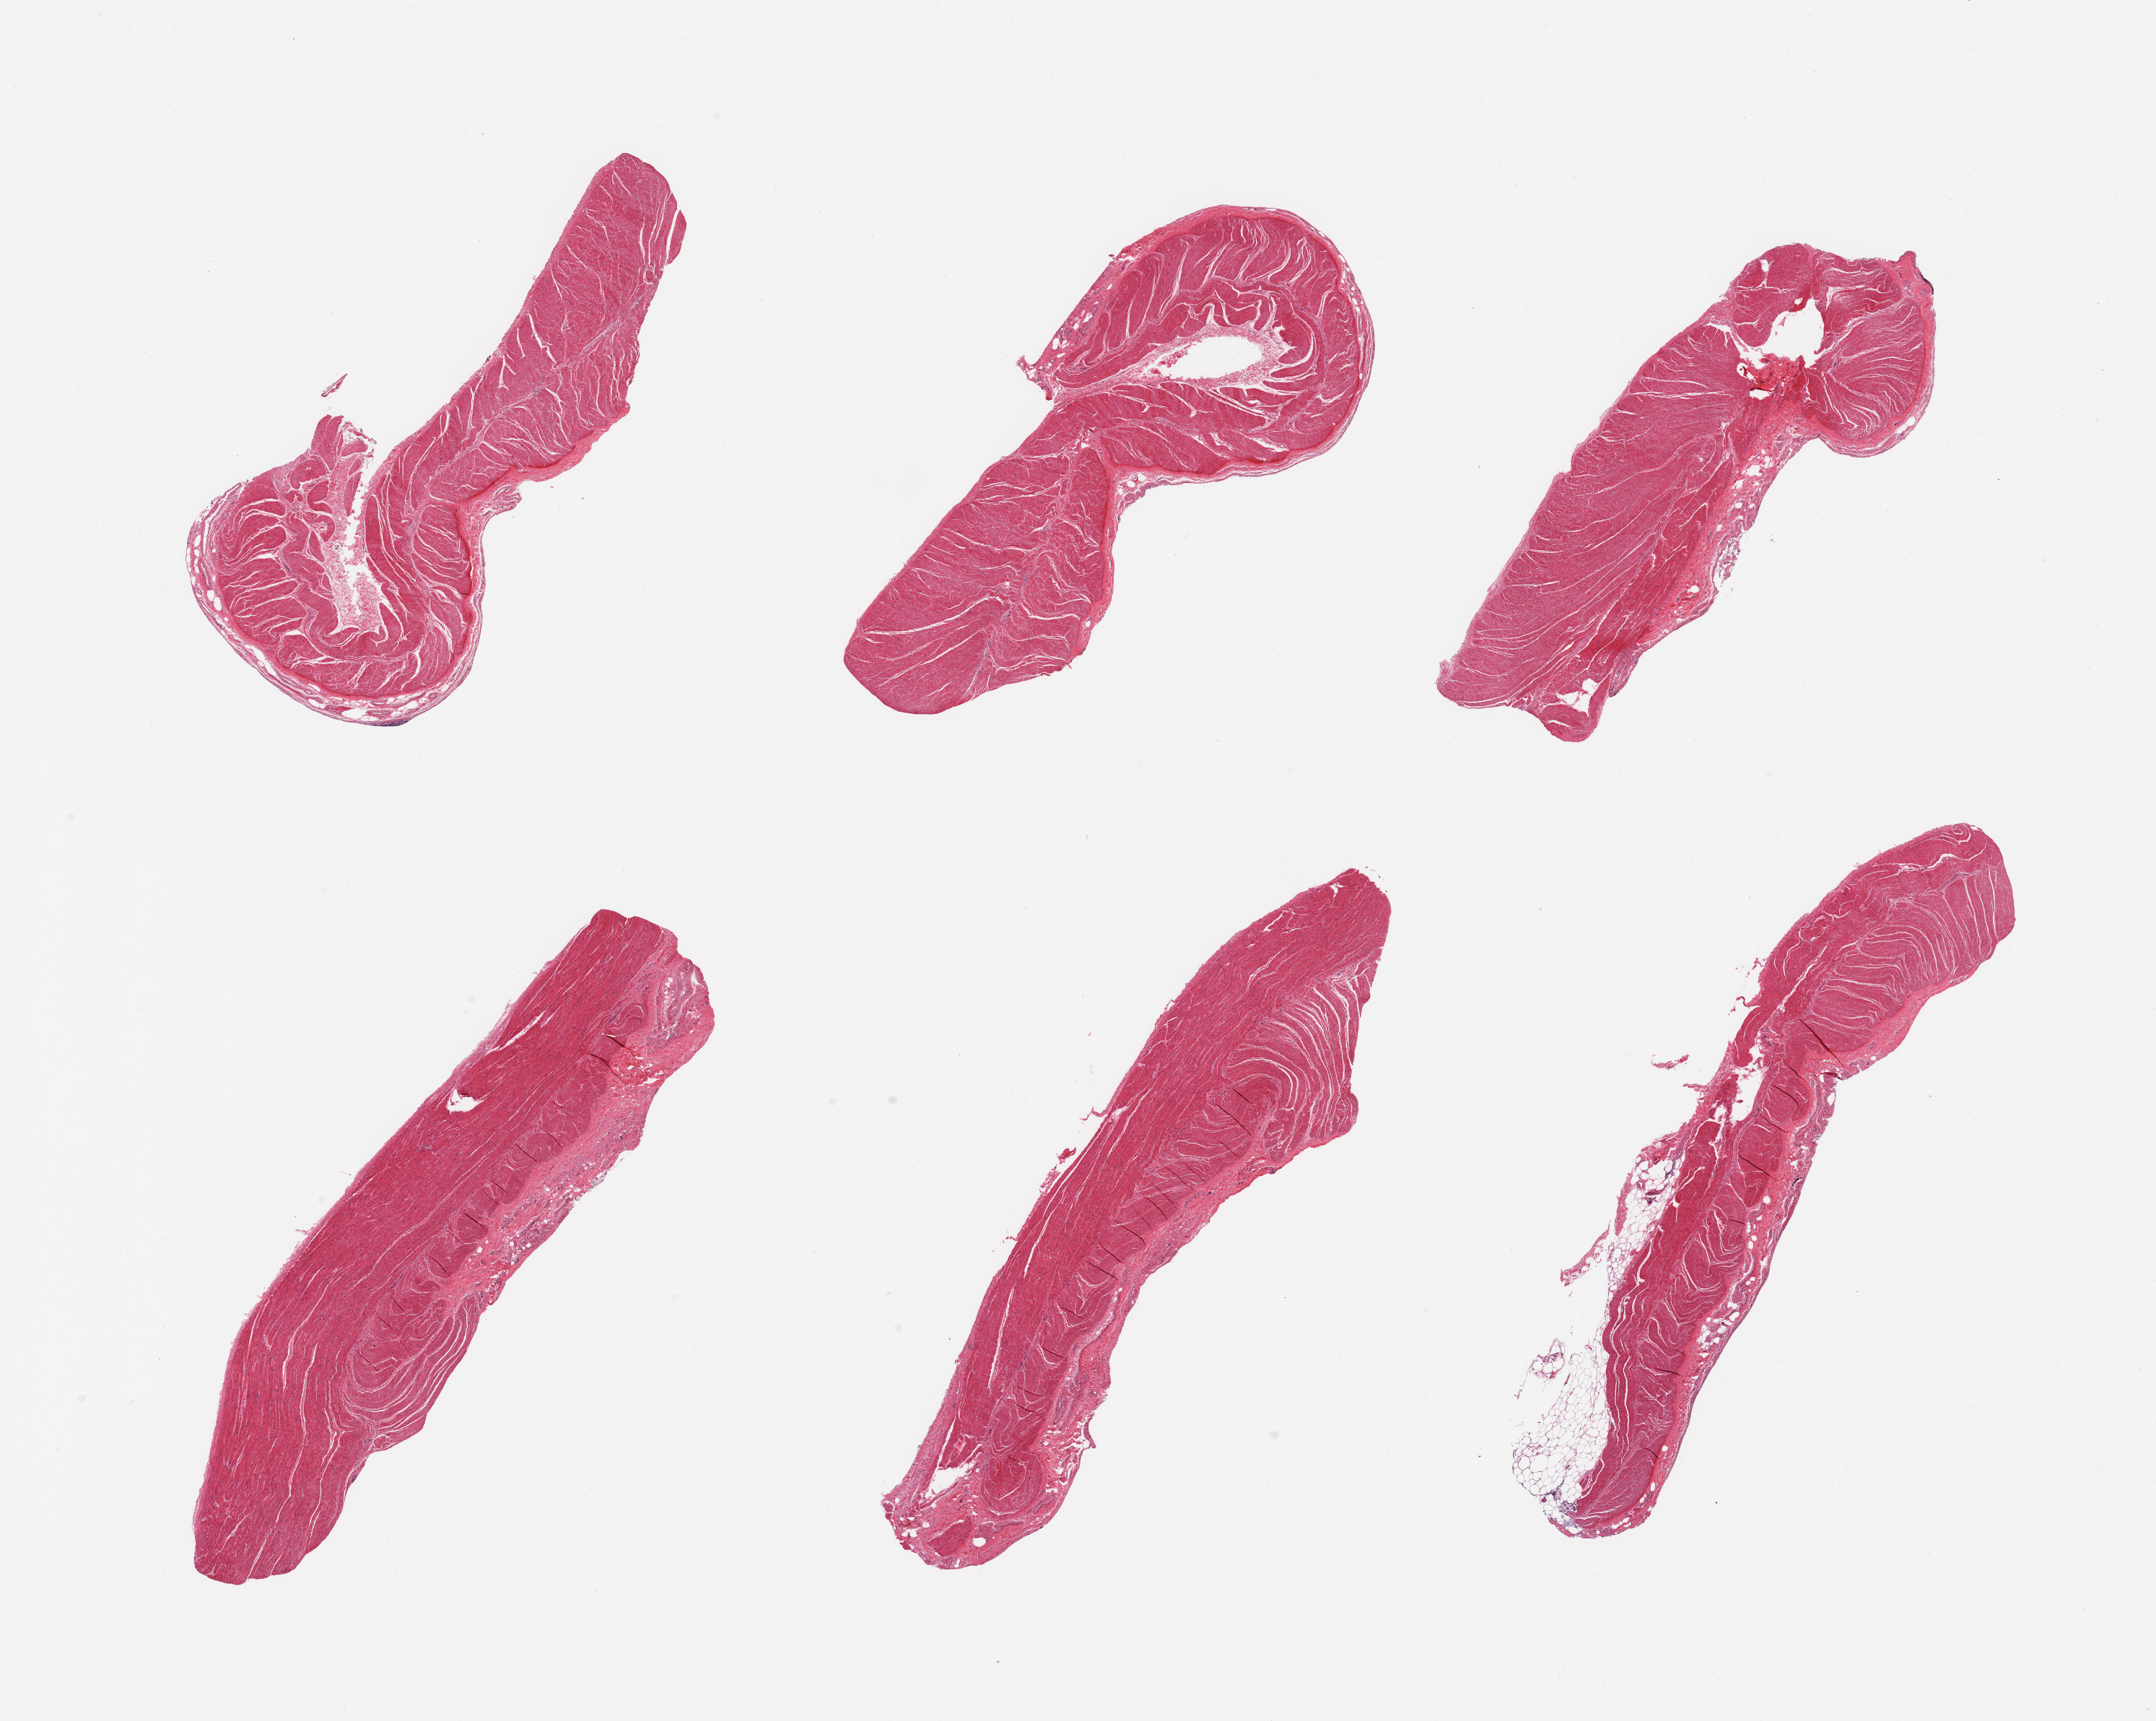
Digitized hematoxylin and eosin (H&E)-stained section, brightfield — a low-resolution overview of the entire scanned area, about 23.6 x 18.9 mm, PAXgene-fixed paraffin-embedded (PFPE) section, section of sigmoid colon (target tissue), donor tissue sample. Donor: male.
Reviewer comment on this tissue sample: 6 pieces, confirmed target muscularis.